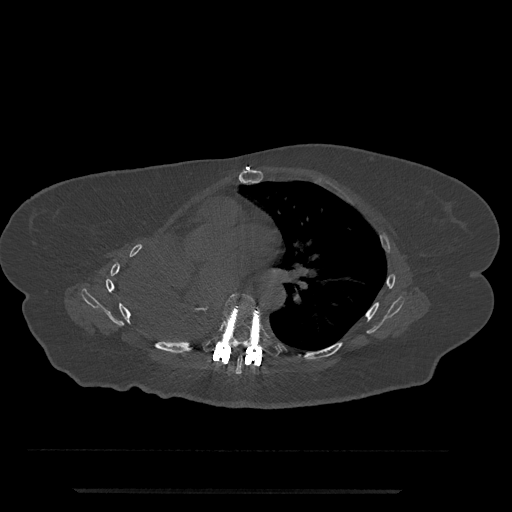
CT including the spine, one axial slice. Slice 457 of 797 in the series (ordered by position). Reconstruction kernel Br40s/3. 120 kVp. Bone window (W 1800 / L 400 HU). 0.5 mm slice thickness. 512 × 512 image matrix, field of view 440 × 440 mm. Female patient, age 51 years. From the clinical record (not read from this slice): primary cancer: neuro; vertebrae with lytic lesions (as recorded): T8.
Annotated regions visible in this slice (semi-automatically segmented with operator editing):
- T6 vertebra: box from (x=235, y=355) to (x=243, y=374) px
- T7 vertebra: (x=203, y=293)–(x=281, y=358)